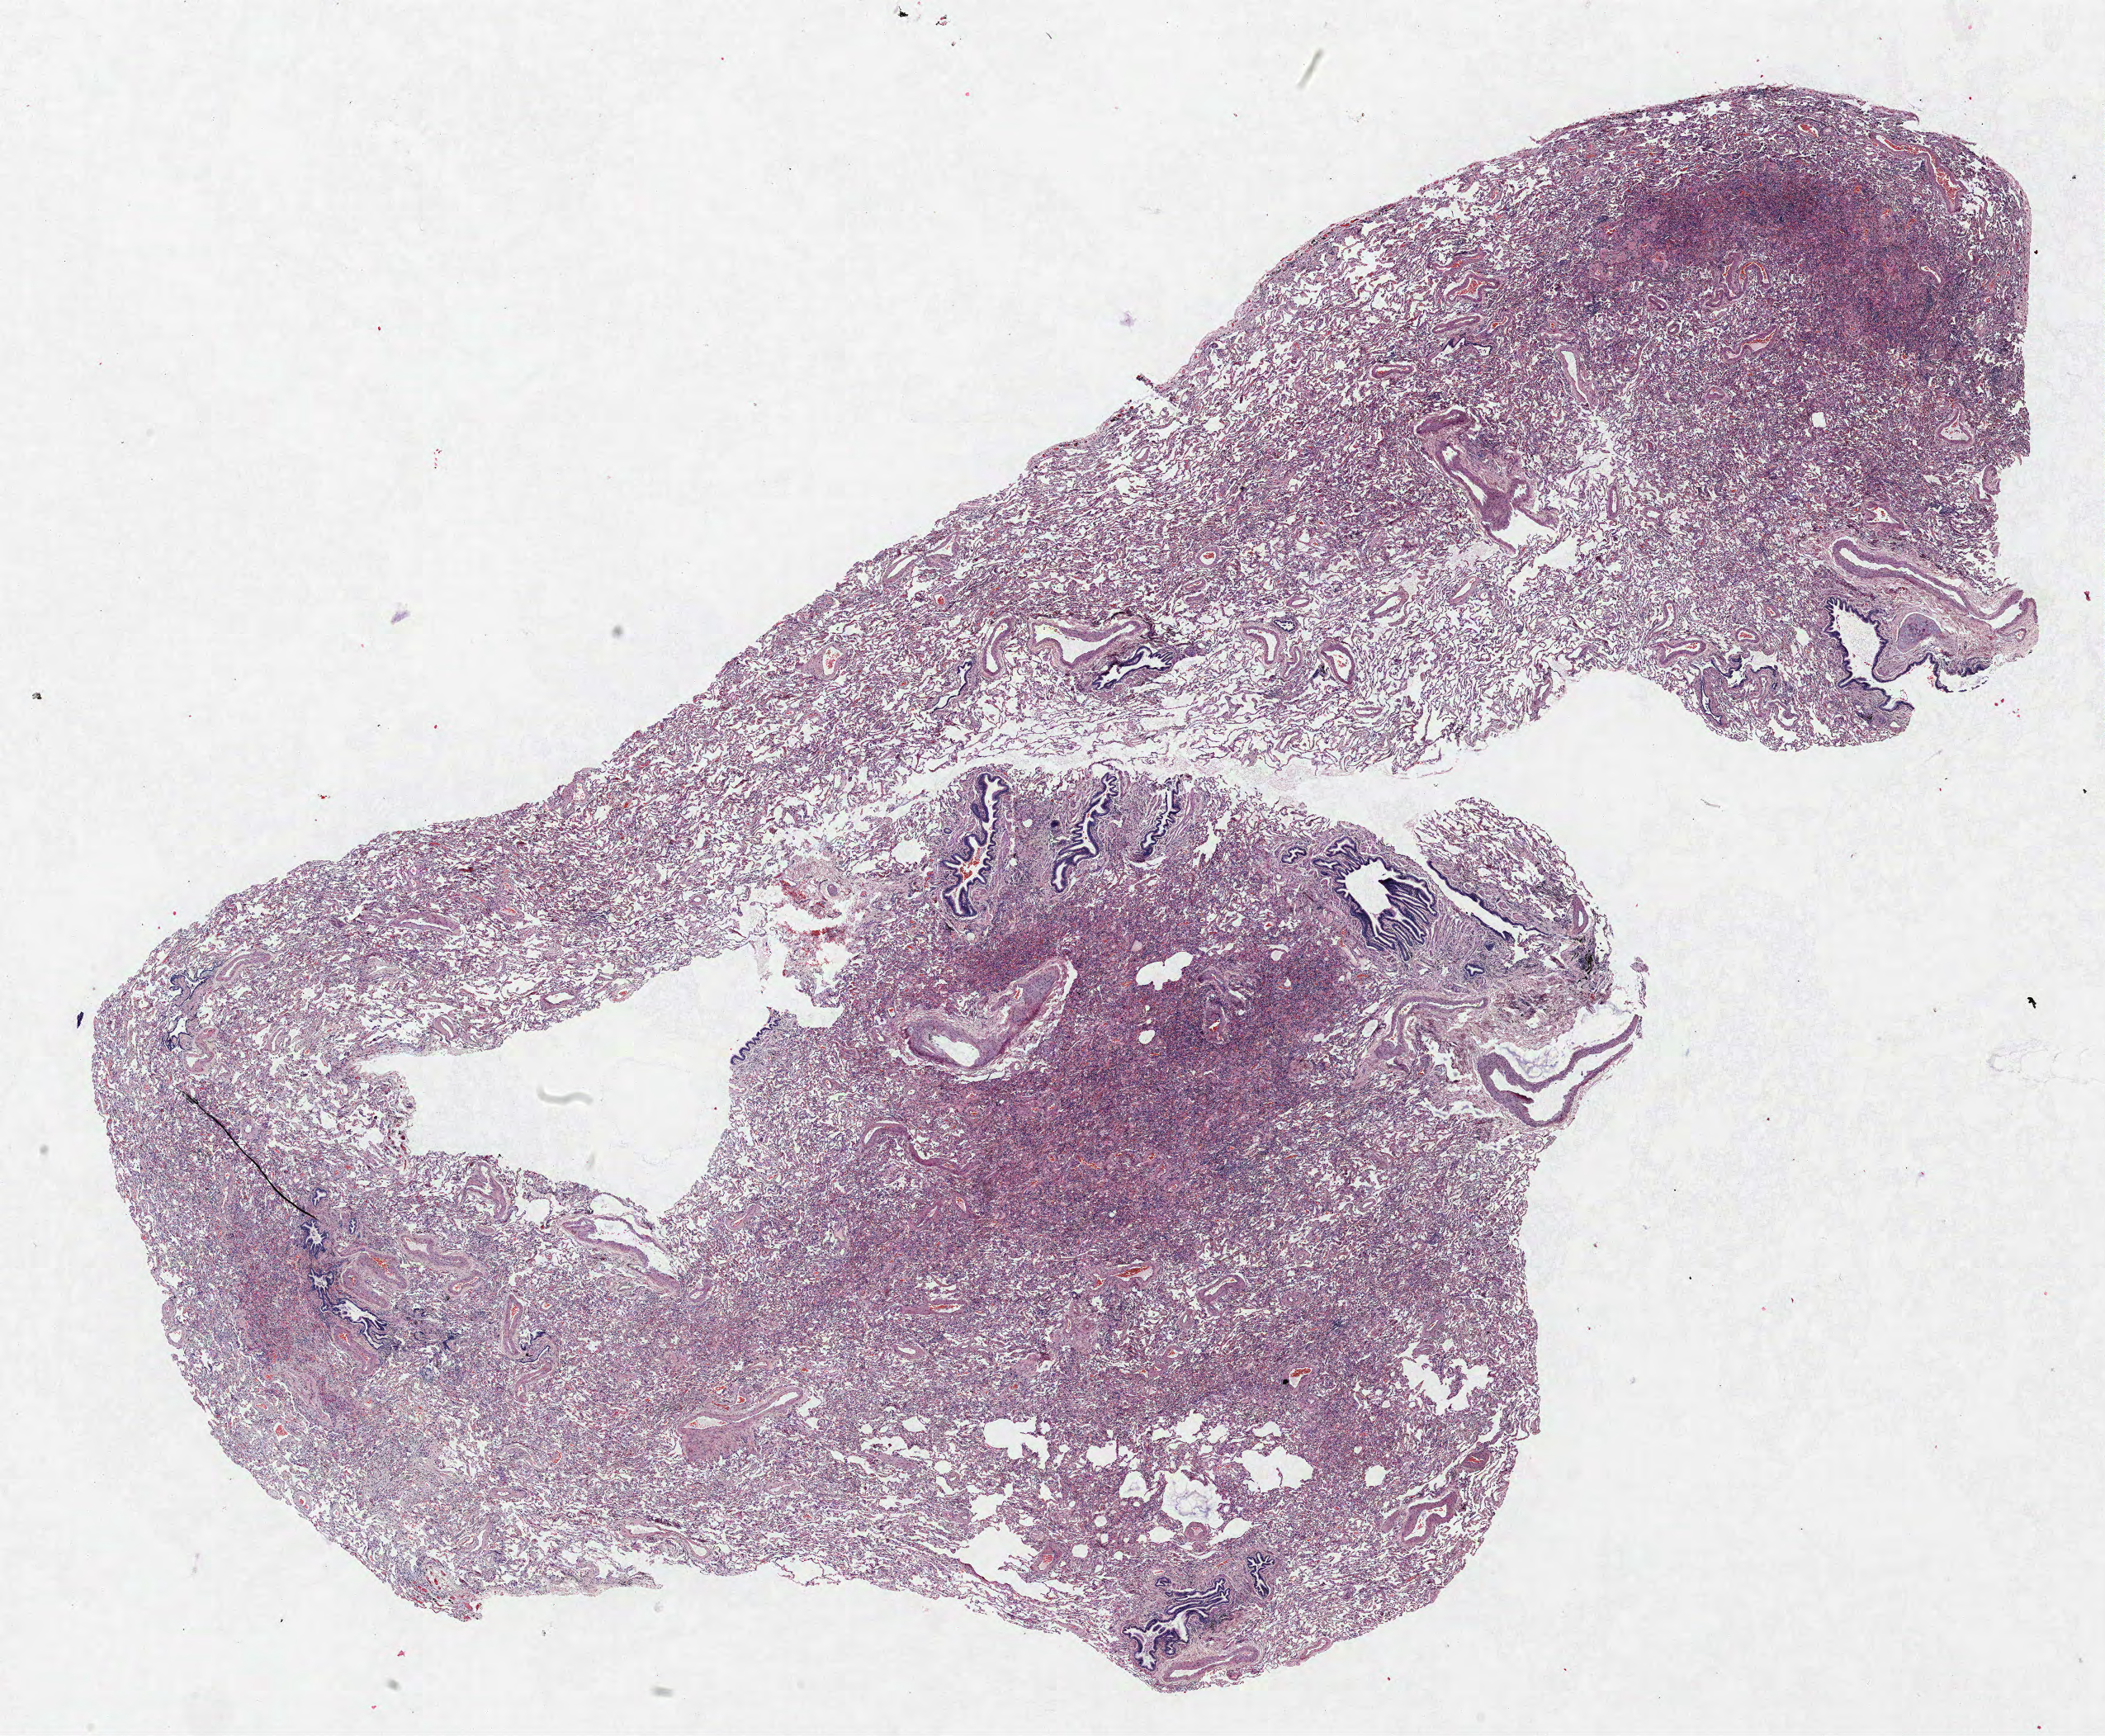
Whole-slide histology image, H&E-stained — low-resolution overview of the scanned area, about 20.4 x 16.8 mm, FFPE section, lung tissue. Male, age 62 at enrolment. Former smoker at enrolment. Grade: poorly differentiated (G3).
• stage (AJCC 6th edition): IB
• primary tumour location (clinical record): right lower lobe
• tumour size (pathology): 45 mm
• participant's lung-cancer diagnosis: Squamous cell carcinoma, NOS (ICD-O-3 8070/3)